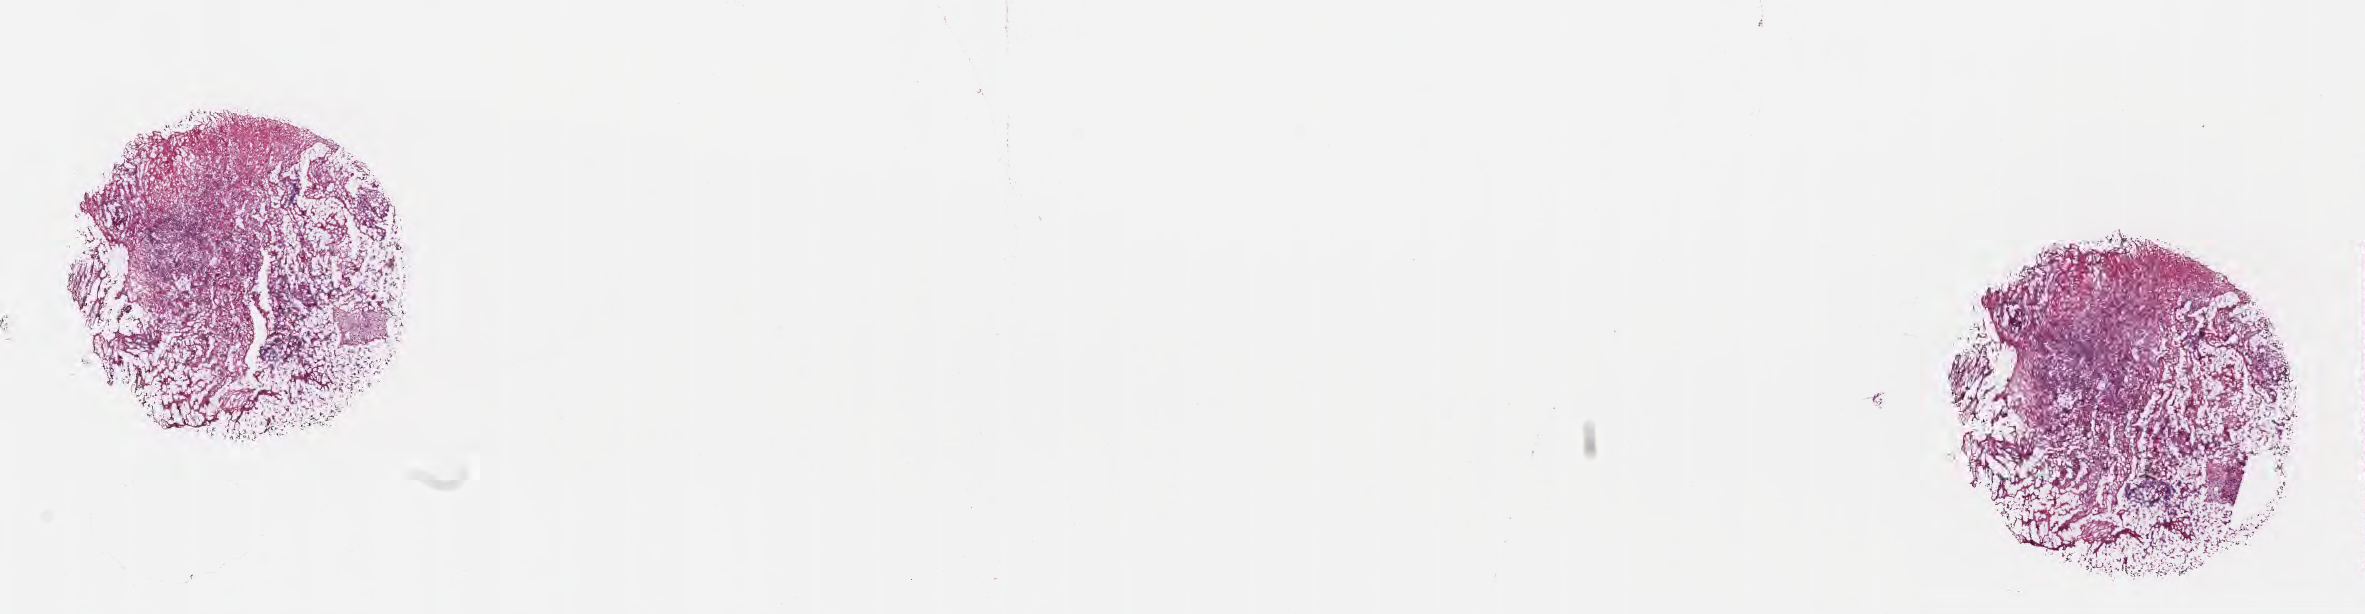
Whole-slide image, haematoxylin and eosin stain, whole scanned area (about 19.1 x 5.0 mm) shown as a low-resolution overview, cryosection, specimen: primary tumor, site: rectosigmoid junction. Female patient; age at initial diagnosis 68 years. Tumor grade: G2 (moderately differentiated). Composition of this section per pathologist review: tumor cells 75%, tumor nuclei 75%, stromal cells 25%, necrosis 0%, normal cells 0%. Infiltration values recorded for this section: lymphocyte infiltration 5%, monocyte infiltration 3%, neutrophil infiltration 8%.
* section: bottom of the tissue portion
* AJCC pathologic stage: Stage IIIB
* histologic diagnosis: Adenocarcinoma, NOS